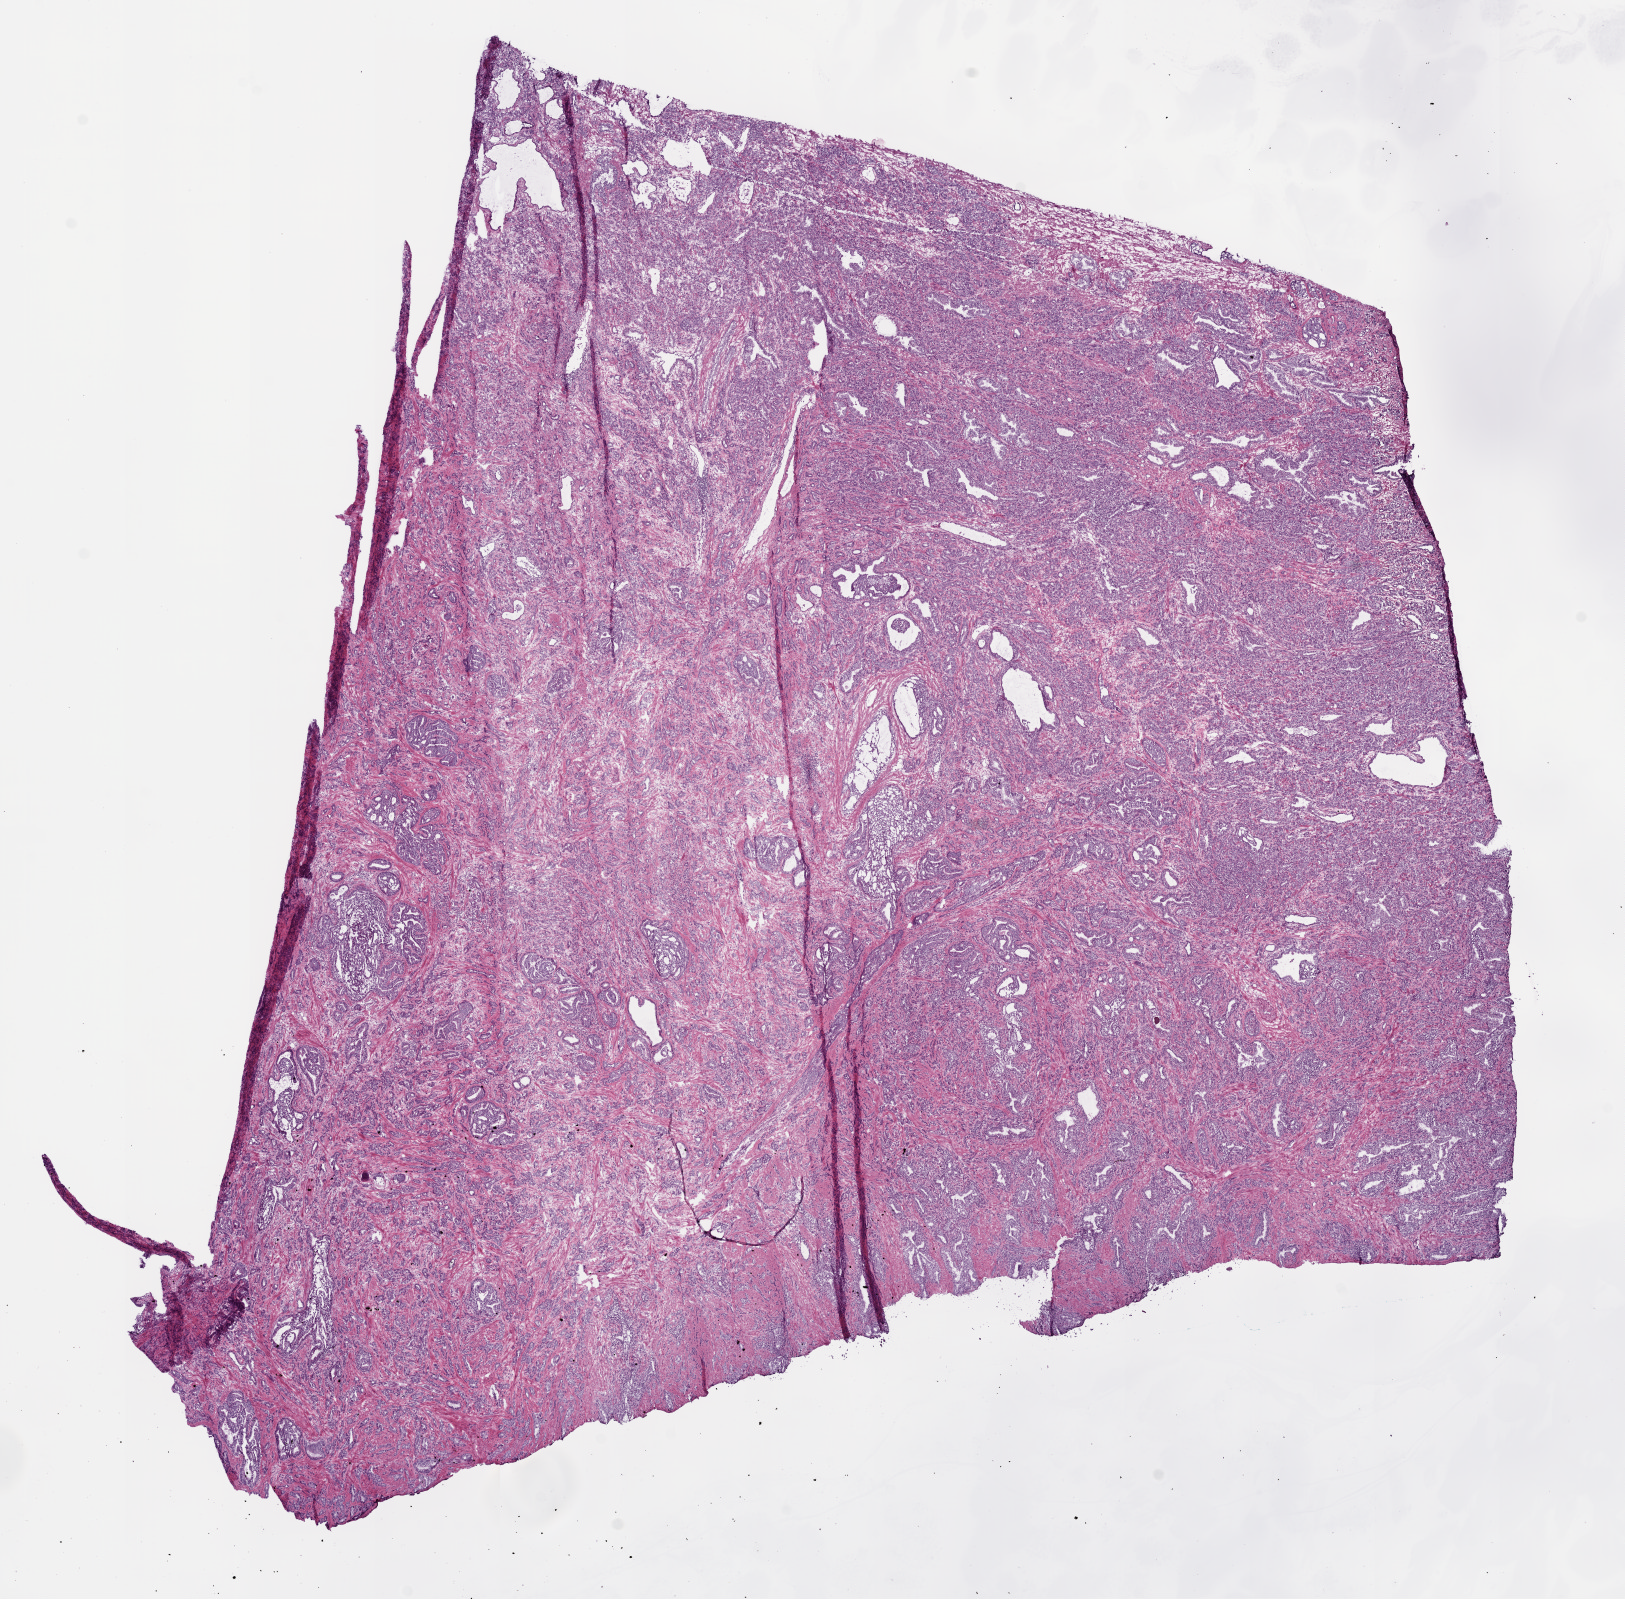
Digitized H&E-stained tissue section (whole slide) — low-resolution overview of the scanned area, about 13.0 x 12.8 mm, frozen section from the bottom of the tissue portion, primary tumour sample from the prostate. Male patient; age at initial diagnosis 67 years. Gleason score: 8 (5+3). Slide review estimates, as recorded: tumour cells 65%, tumour nuclei 80%, normal cells 10%, stromal cells 25%, necrosis 0%. Inflammatory infiltration, as recorded: lymphocyte infiltration 2%, monocyte infiltration 0%, neutrophil infiltration 0%.
• laterality: bilateral
• lymph nodes positive (case pathology): 1 of 7 examined
• histologic diagnosis: Acinar cell carcinoma